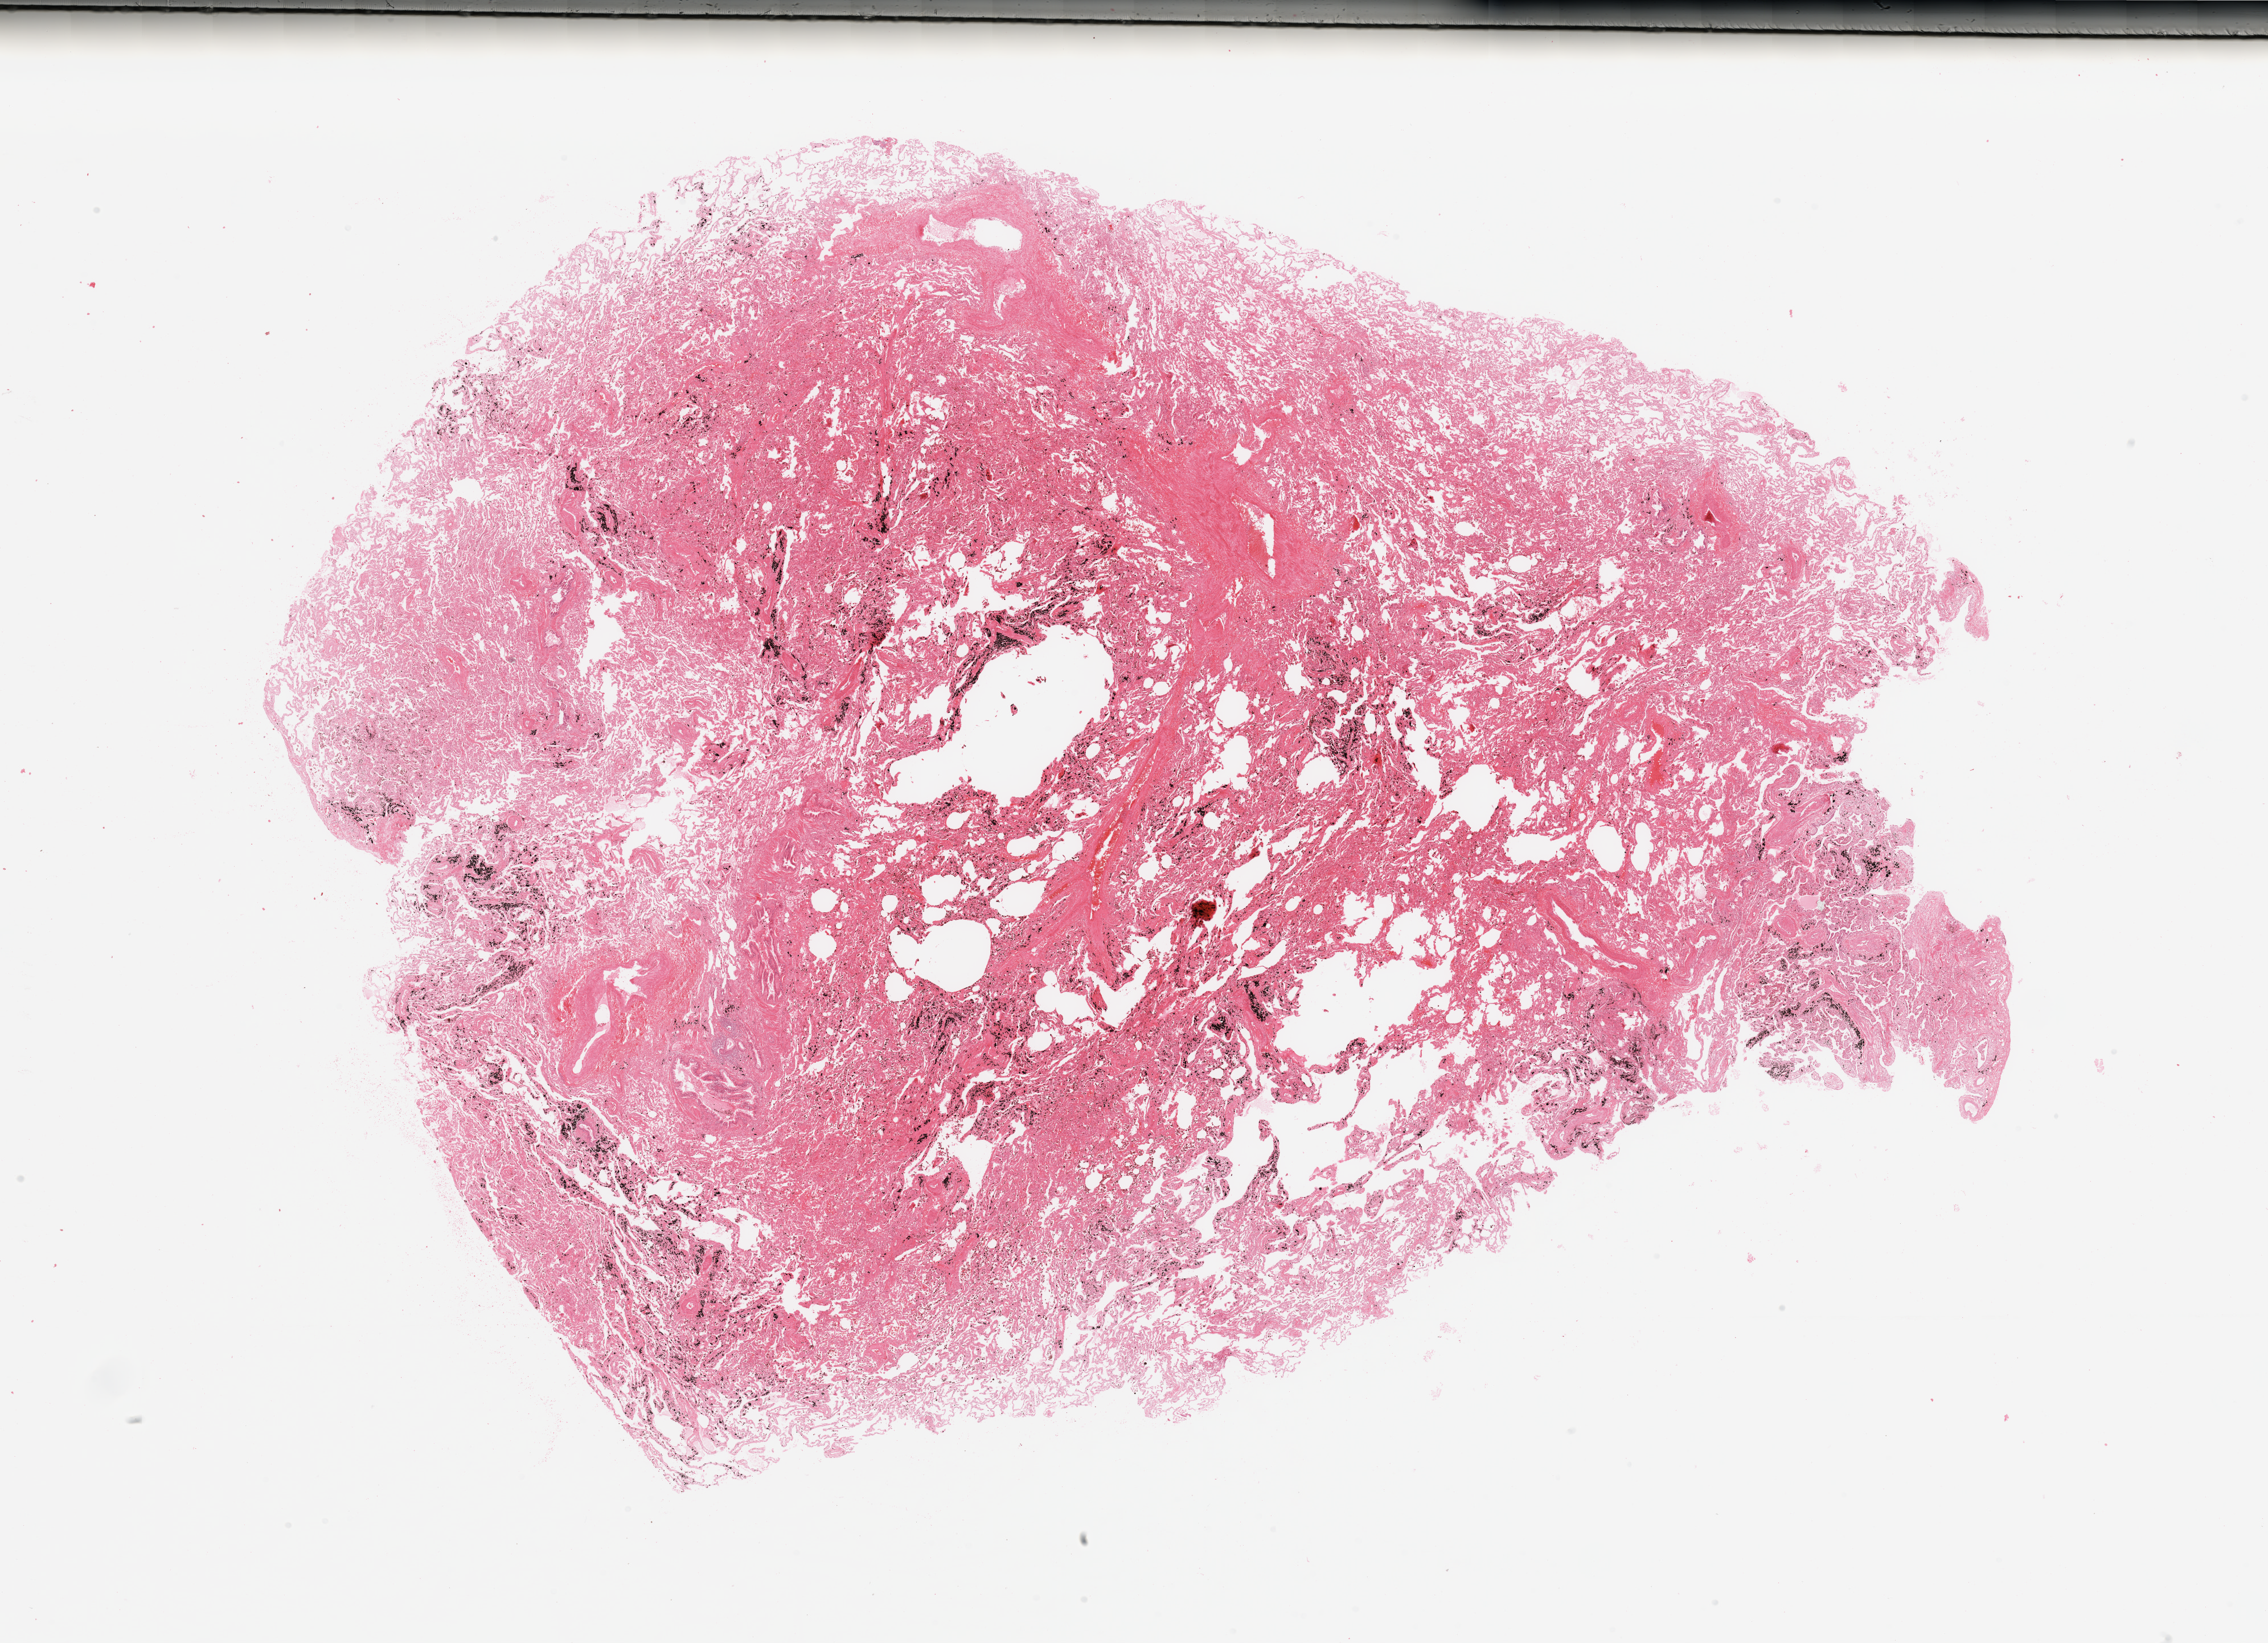
H&E whole-slide image, a low-resolution overview of the entire scanned area, about 31.5 x 22.8 mm, normal (non-tumour) tissue sample, sampled site: lung. Male, 54 y/o.
* this section: normal (non-tumour) tissue from the same patient
* patient diagnosis: Adenocarcinoma, NOS